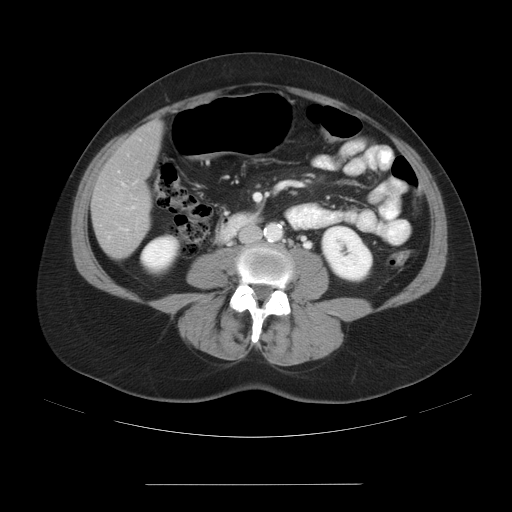
Contrast-enhanced abdominal CT, one axial slice. Slice 5 of 27 in the series (ordered by position). Reconstruction kernel STANDARD. Intravenous contrast given. Soft-tissue window (W 400 / L 40 HU). 7.5 mm slice thickness. 512 × 512 image matrix, field of view 440 × 440 mm. Female patient, age 58 years. Case-level facts recorded for this patient, not image findings: diagnosis: colorectal cancer liver metastases, imaged before liver resection; multiple liver metastases: yes; largest metastasis: 1.9 cm; disease in both lobes: yes.
Outlined on this slice (expert manual segmentation):
- liver: bounding box <92,123,161,259> (left, top, right, bottom; pixels)
- planned liver remnant (the part of the liver to remain after resection): <101,124,161,186>
- portal vein (with intrahepatic branches): <117,170,127,188>